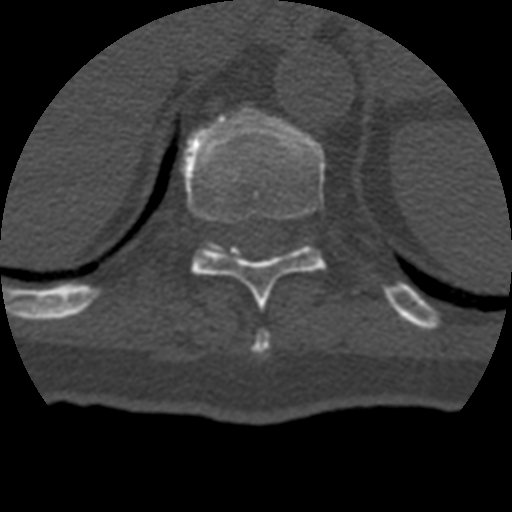
CT including the spine, one axial slice. Reconstruction kernel STANDARD. 120 kVp. Bone window (W 1800 / L 400 HU). 1.25 mm slice thickness. 512 × 512 image matrix. Patient age 69 years. Case-level facts recorded for this patient, not image findings: primary cancer: prostate.
Annotated regions visible in this slice (semi-automatically segmented with operator editing):
- T10 vertebra: bounding box <182,111,326,308> (left, top, right, bottom; pixels)
- T9 vertebra: <253,330,271,354>